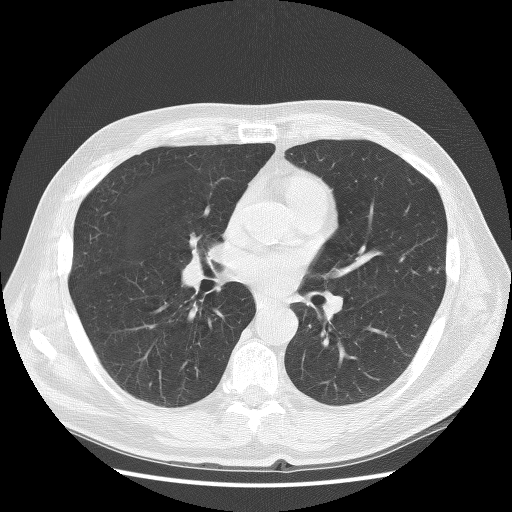
Low-dose screening chest CT, axial slice, baseline annual screen, lung window (W 1500 / L -600 HU), 2.5 mm slice thickness, slice 120 of 272 in the series, 512 × 512 image matrix, field of view 360 × 360 mm. Male participant, aged 67 years at enrolment. Former smoker at enrolment.
- Expert reader's lesion annotation, bounding box [x1, y1, x2, y2] px = [406, 247, 463, 294].
- Screening reader's record for this exam: no non-calcified nodule ≥4 mm recorded.
- Participant outcome: lung cancer diagnosed 772 days after this screen (after the third annual screen) — squamous cell carcinoma, NOS, left upper lobe, moderately differentiated (G2), stage IB (AJCC 6th edition), 25 mm at pathology.